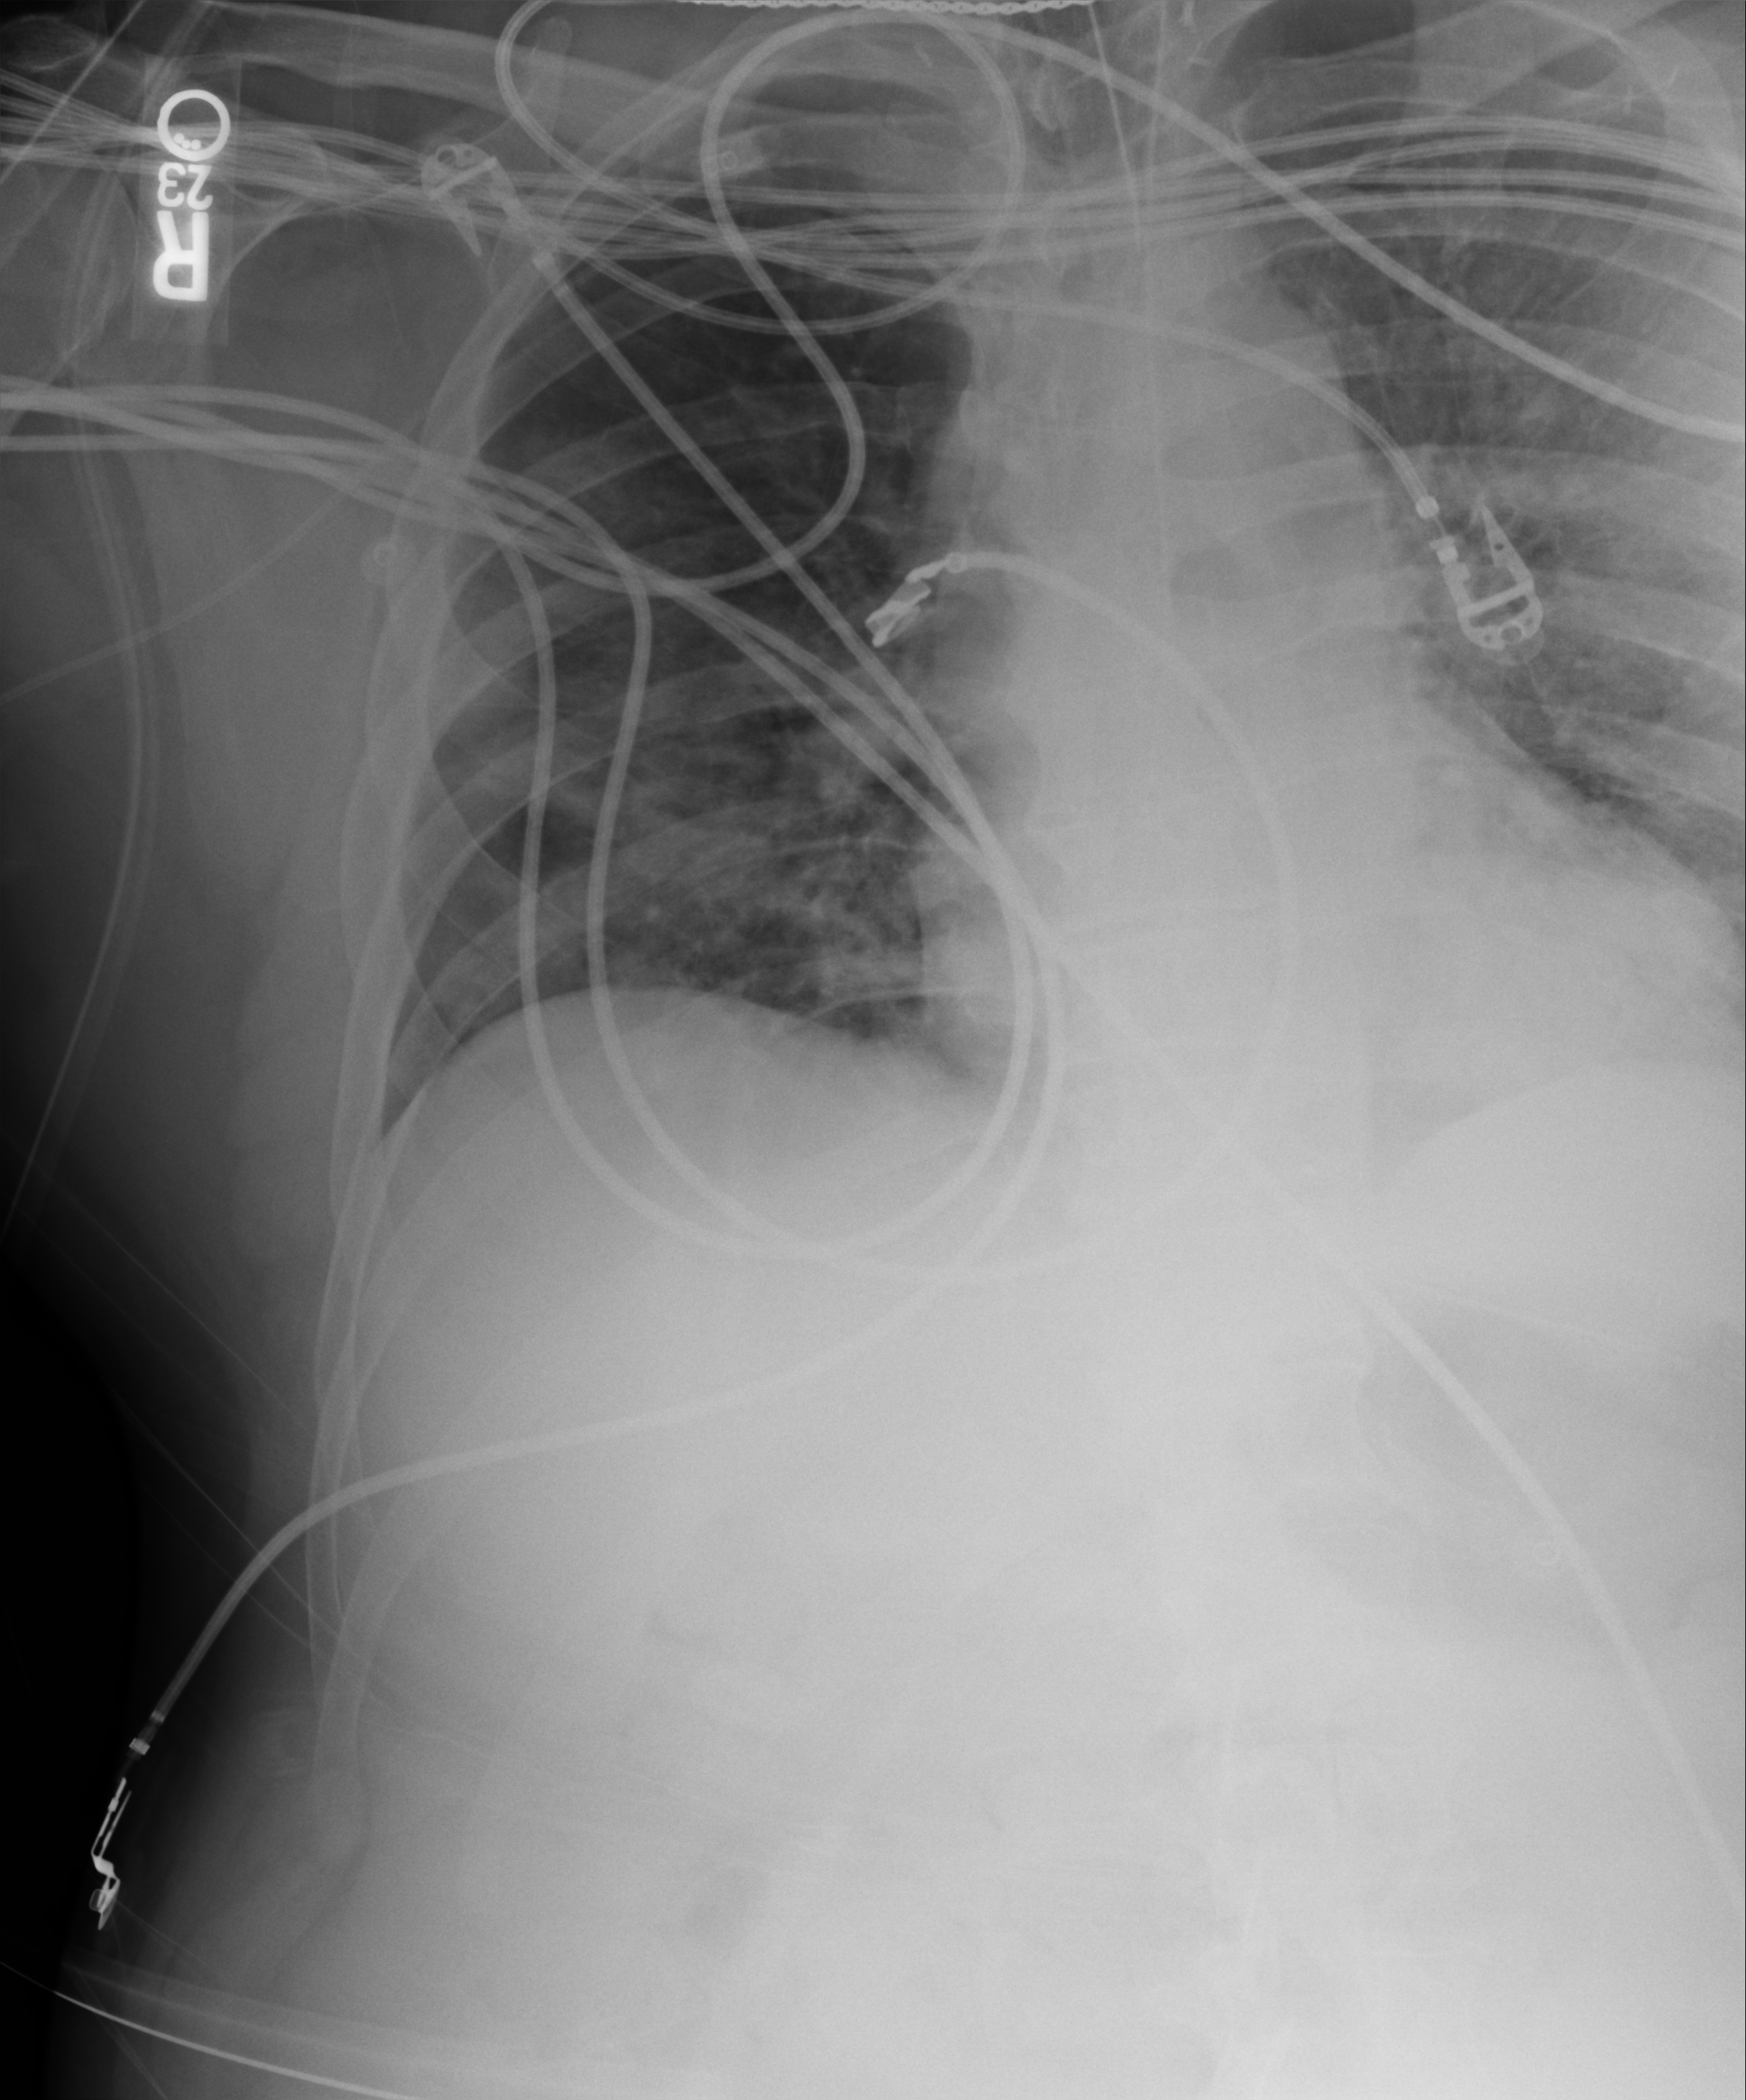
Bedside chest radiograph (computed radiography); anteroposterior (AP) projection. Patient hospitalised with COVID-19, aged 18–59 years.
Hospital-stay facts (about this admission, not read from this image; timing relative to this image not recorded): mechanically ventilated during this hospital stay: yes; hypertension (admission record): no.